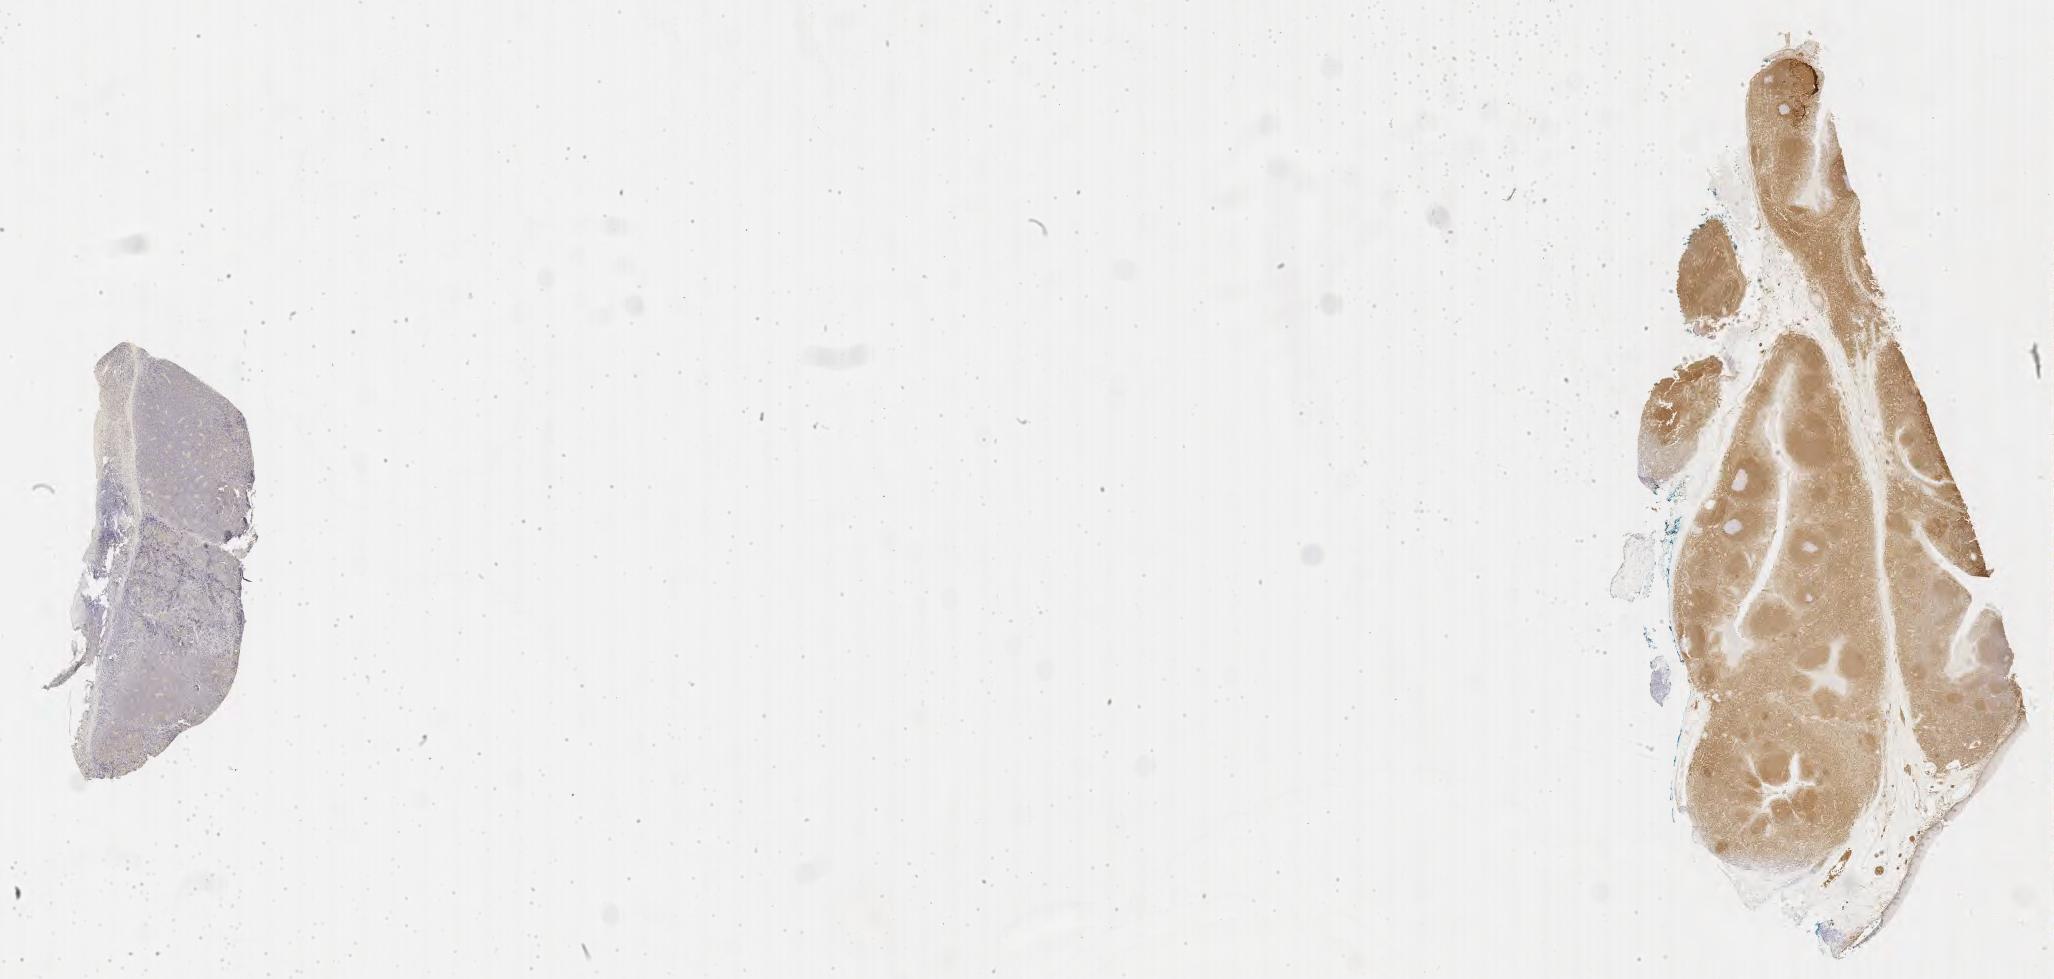
IHC for BCL2, whole-slide image, shown as a low-resolution overview of the whole scanned area (about 33.2 x 15.8 mm). Tumor tissue. Anatomic site: testis. Patient: male, age at initial diagnosis 8 years.
- diagnosis: Burkitt lymphoma, NOS